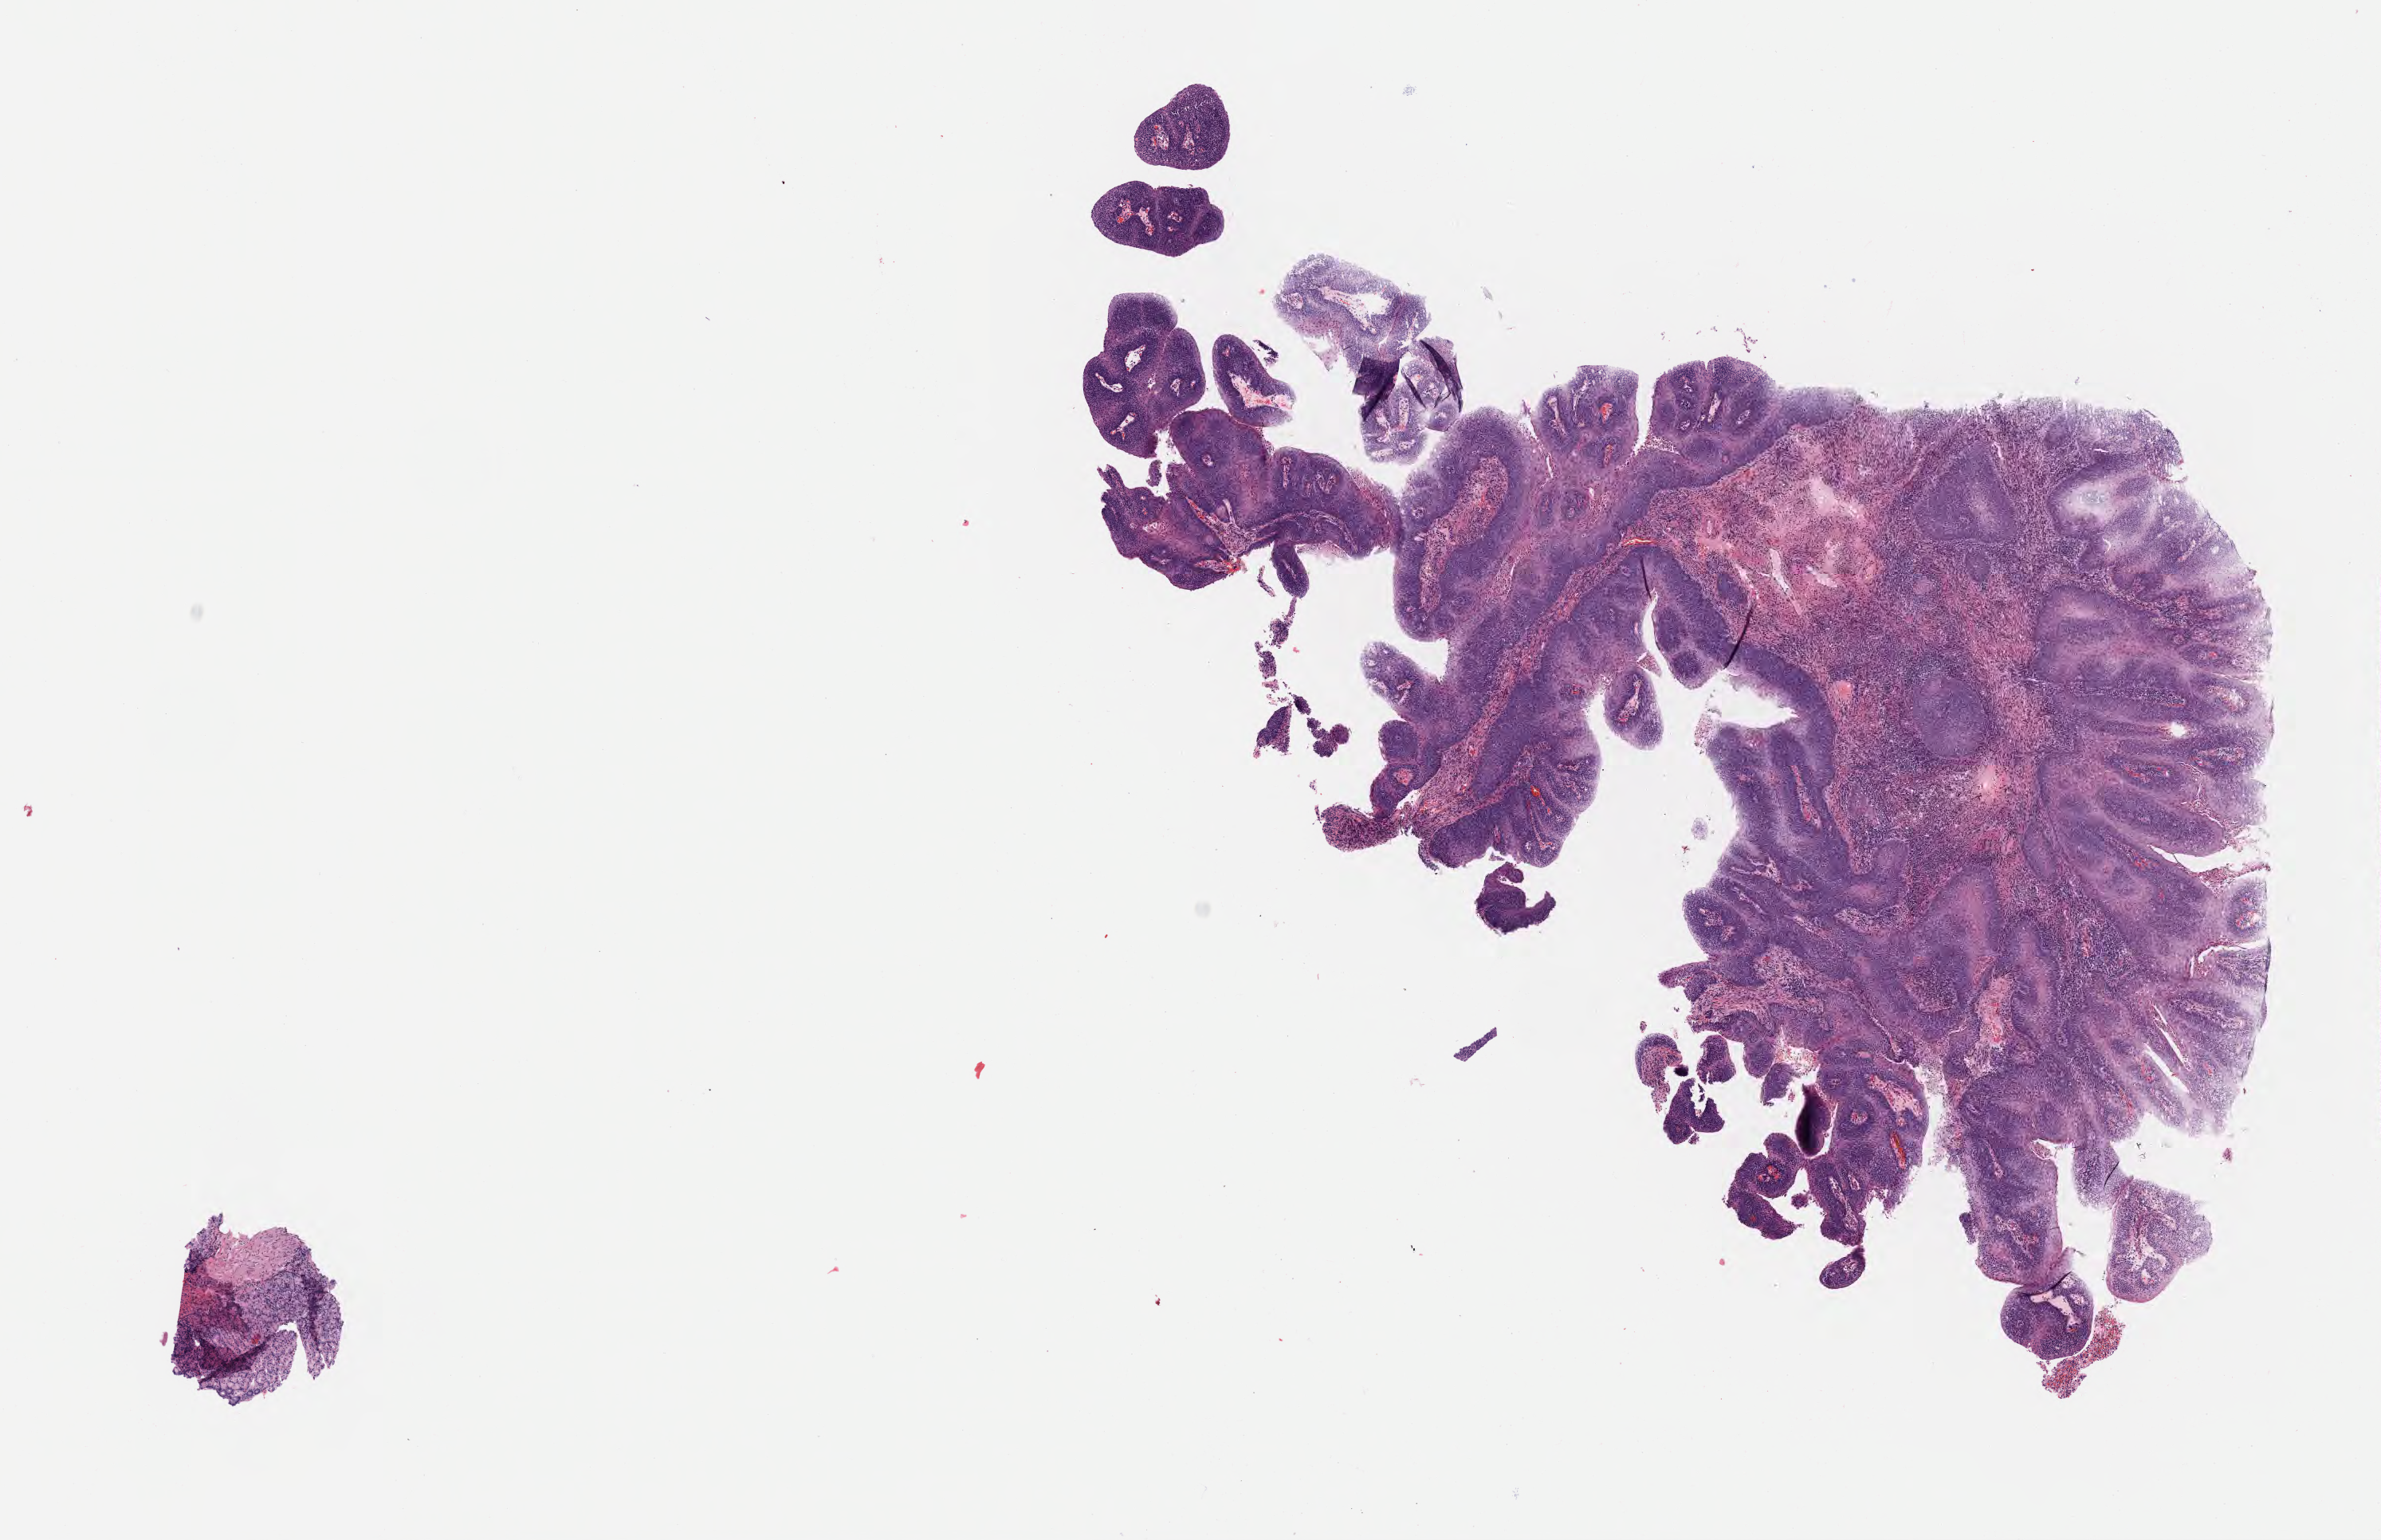
Whole-slide image, hematoxylin and eosin (H&E) stain, low-resolution overview of the scanned area, about 12.1 x 7.8 mm; tumor tissue; anatomic site: cervix. Patient: female, age 40 years.
Histologic diagnosis: Squamous cell carcinoma, NOS.